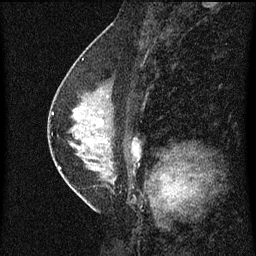
Breast MRI (dynamic contrast-enhanced), one sagittal slice. Slice 33 of 60 in the series (ordered by position). Dynamic contrast-enhanced series, image 2 of 3 at this slice position (ordered by acquisition). 1.5 T. TE 4.2 ms, TR 8 ms. 2 mm slice thickness. 256 × 256 image matrix, field of view 180 × 180 mm. Patient: female, 47 years.
Annotated regions visible in this slice (semi-automatic segmentation, software-assisted and operator-edited):
- analysis volume of interest (the breast-tissue region the enhancement analysis was run in; not a lesion): bounding box <54,80,140,187> (left, top, right, bottom; pixels)
- tumour enhancement mask (voxels above the 70 % enhancement threshold inside the analysis volume of interest): <60,148,137,169>